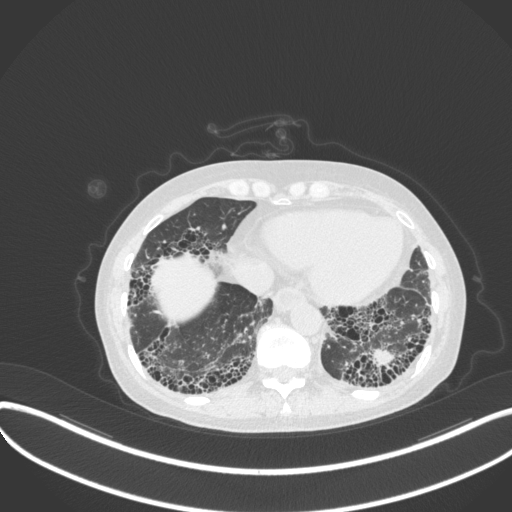
Chest CT, one axial slice. Slice 72 of 373 in the series (ordered by position). Reconstruction kernel B31f. 120 kVp. Lung window (W 1500 / L -600 HU). 1 mm slice thickness. 512 × 512 image matrix, field of view 400 × 400 mm. Patient: female, 56 years. From the clinical record (not read from this slice): clinical TNM (as recorded): T1 N0 M0.
Annotated regions visible in this slice (bounding box drawn by a radiologist):
- lung tumour (recorded histology: adenocarcinoma): bounding box <368,345,398,369> (left, top, right, bottom; pixels)